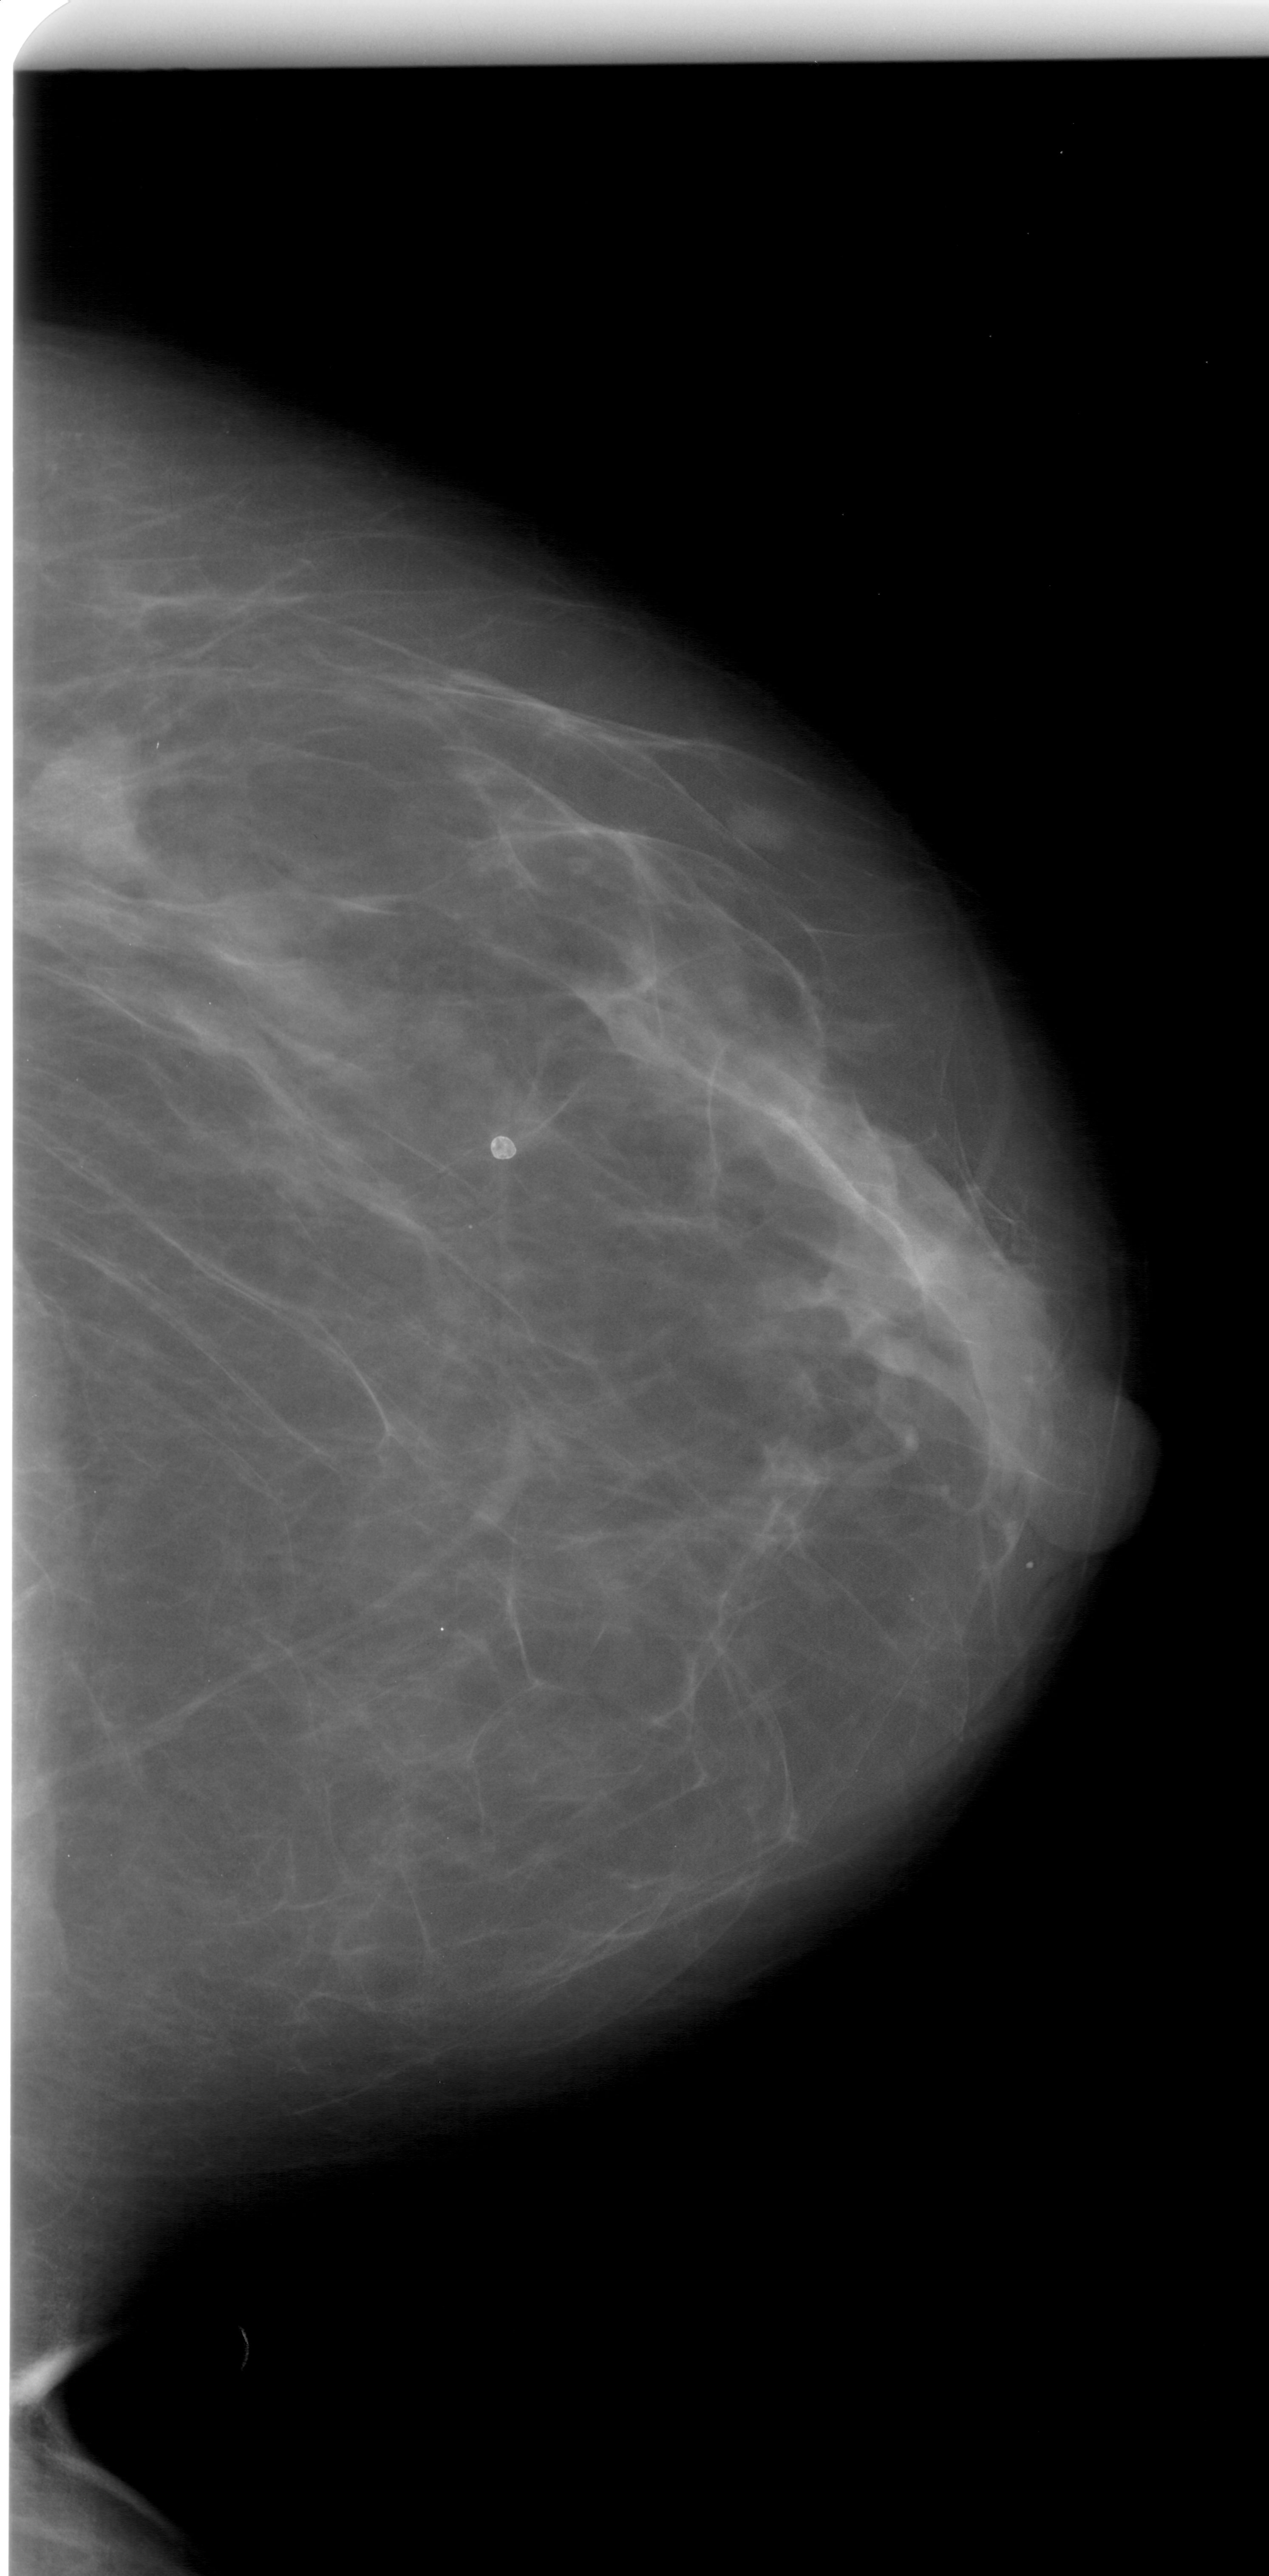
Digitized screen-film mammogram; right breast; CC view; breast composition: almost entirely fatty (BI-RADS density category 1 of 4); 1269 × 2576 image matrix.
Expert-marked regions of interest on this film, with their recorded descriptors:
- mass, shape lobulated, margins ill defined; BI-RADS assessment category 4; subtlety rating 4 on a 1 (subtle) to 5 (obvious) scale; pathology (as recorded): benign: bounding box [x1, y1, x2, y2] px = [17, 726, 159, 896]